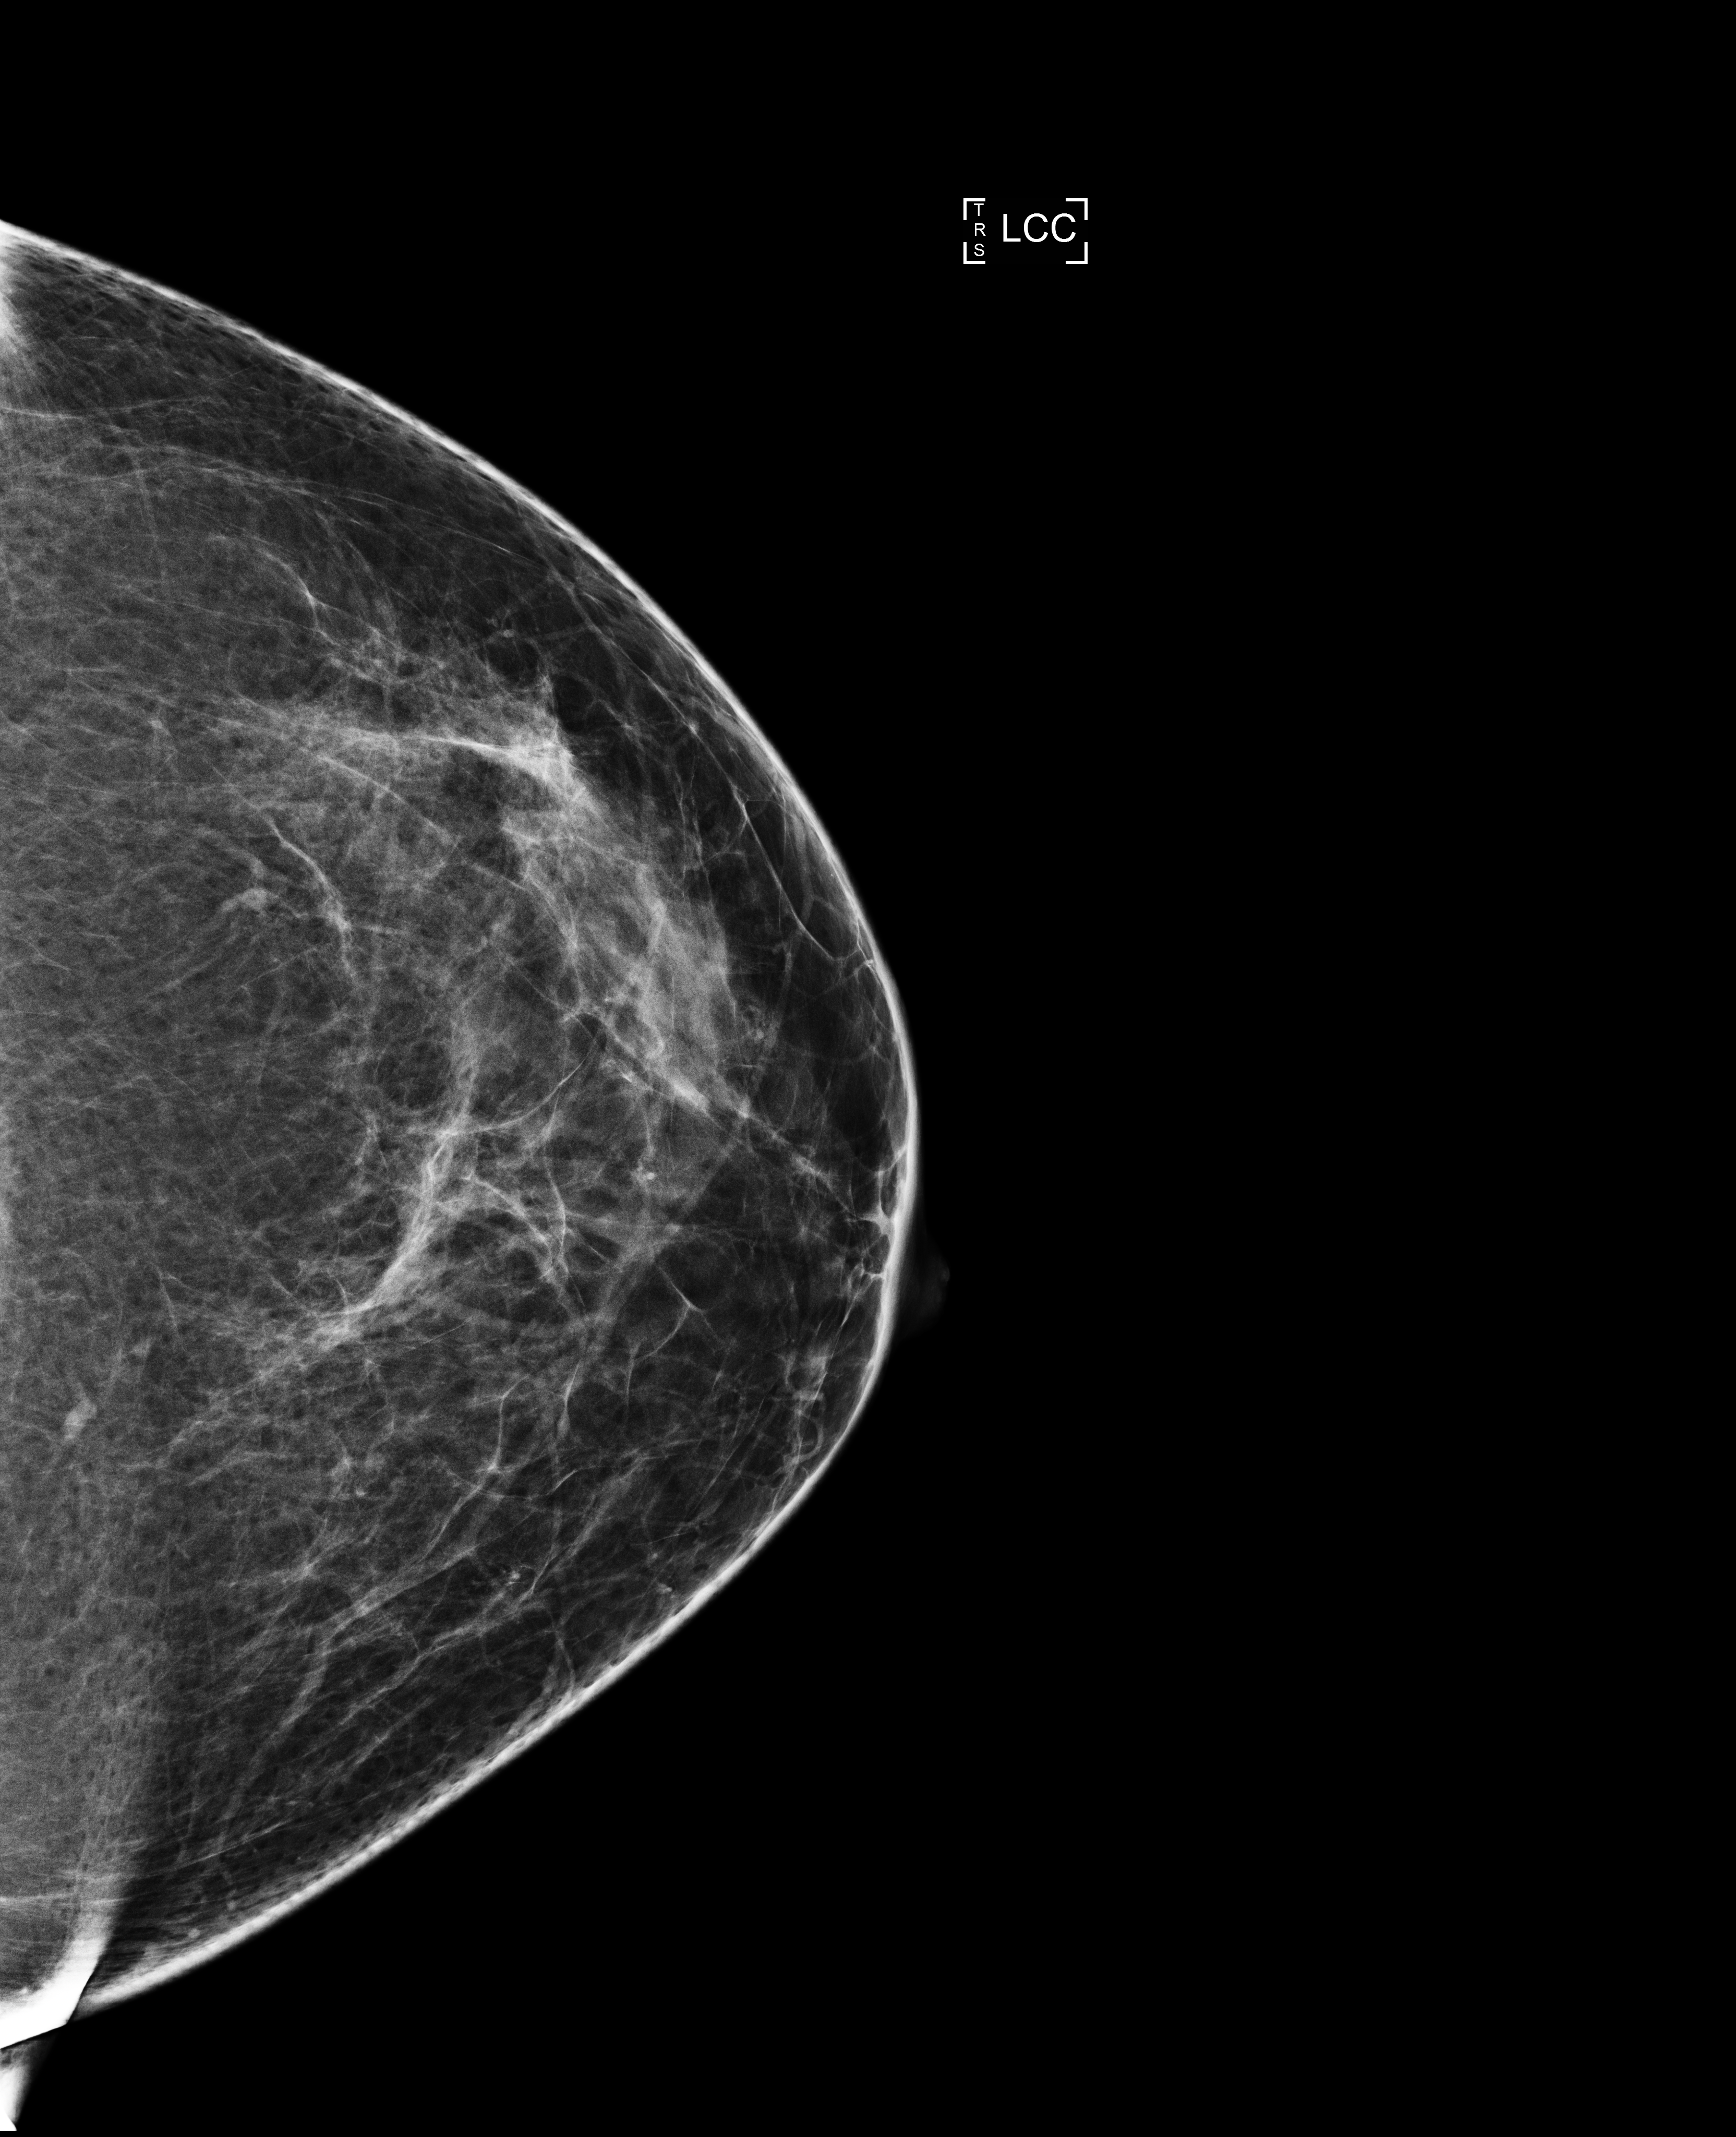
Screening examination, compressed breast thickness 59 mm. Patient aged 47 years (female).
Image type: full-field digital mammogram. Breast: left. Projection: craniocaudal (CC) view.